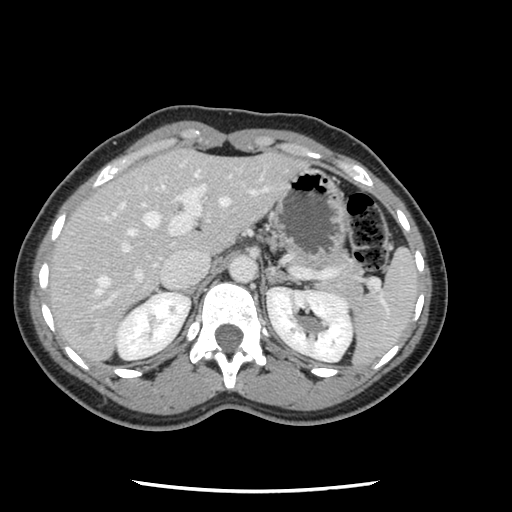
Contrast-enhanced abdominal CT, one axial slice. Position 80 of 134 along the scan axis. 120 kVp. Intravenous contrast given. Soft-tissue window (W 400 / L 40 HU). 512 × 512 image matrix, field of view 330 × 330 mm. Female patient, age 43 years. From the clinical record (not read from this slice): diagnosis: colorectal cancer liver metastases, imaged before liver resection; multiple liver metastases: yes; largest metastasis: 3.4 cm.
Outlined on this slice (outlined manually by an expert reader):
- hepatic veins: box from (x=95, y=171) to (x=231, y=295) px
- liver: (x=48, y=151)–(x=302, y=363)
- planned liver remnant (the part of the liver to remain after resection): (x=48, y=154)–(x=190, y=306)
- portal vein (with intrahepatic branches): (x=92, y=185)–(x=269, y=310)
- liver metastasis: (x=73, y=326)–(x=91, y=335)